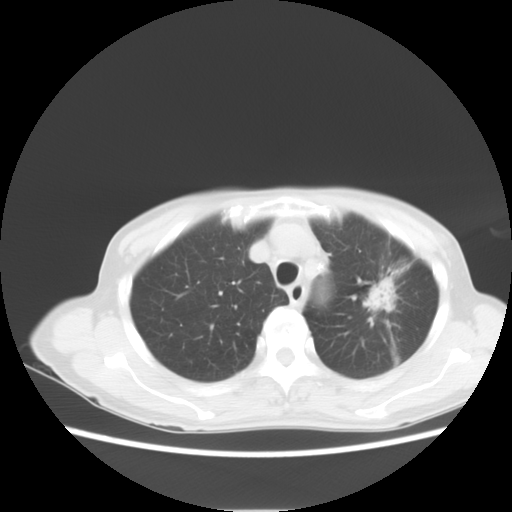
Chest CT, one axial slice. Slice 8 of 14 in the series (ordered by position). Reconstruction kernel STANDARD. Lung window (W 1500 / L -600 HU). 5 mm slice thickness. 512 × 512 image matrix, field of view 350 × 350 mm. Patient: female, 71 years. From the clinical record (not read from this slice): clinical TNM (as recorded): T2 N0 M0.
Annotated regions visible in this slice (rectangle marked by the reading radiologist):
- lung tumour (recorded histology: adenocarcinoma): box from (x=363, y=274) to (x=397, y=315) px